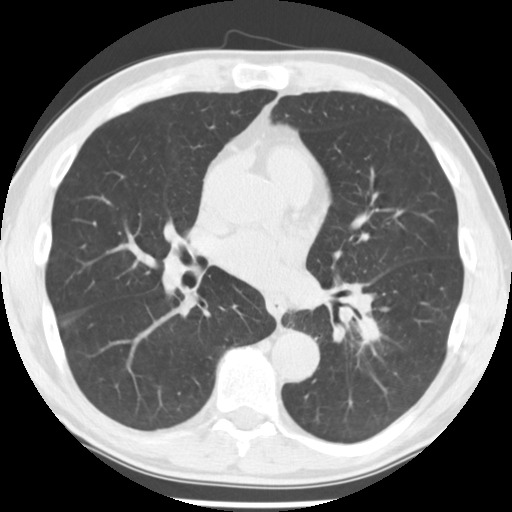
Low-dose screening chest CT, axial slice. Third annual screen. Lung window (W 1500 / L -600 HU). Slice 117 of 242 in the series. 512 × 512 image matrix. Male, age 64 years at enrolment. Current smoker at enrolment.
- Expert-annotated lung lesion, box from (x=350, y=316) to (x=389, y=350) px.
- No non-calcified nodule or mass ≥4 mm was recorded by the screening reader at this exam.
- Participant outcome: lung cancer diagnosed 203 days after this screen — adenocarcinoma, NOS, left lower lobe, stage IV (AJCC 6th edition), 44 mm at pathology.